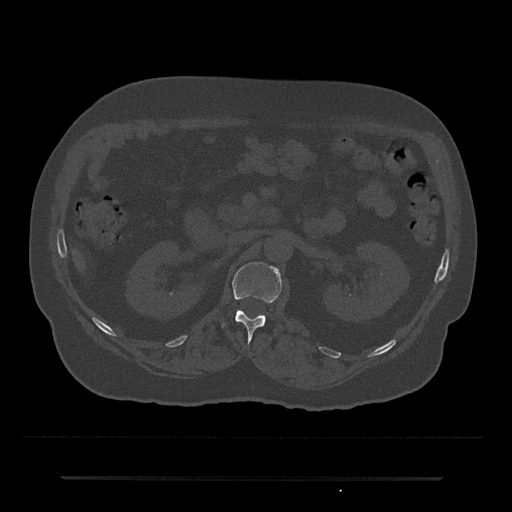
CT including the spine, one axial slice; reconstruction kernel Br40s/3; 120 kVp; bone window (W 1800 / L 400 HU); 0.5 mm slice thickness; 512 × 512 image matrix, field of view 437 × 437 mm. Patient: male, 69 years. Case-level facts recorded for this patient, not image findings: primary cancer: prostate.
Structures marked on this image (semi-automatic segmentation, software-assisted and operator-edited):
- L1 vertebra: bounding box [x1, y1, x2, y2] px = [222, 262, 282, 340]